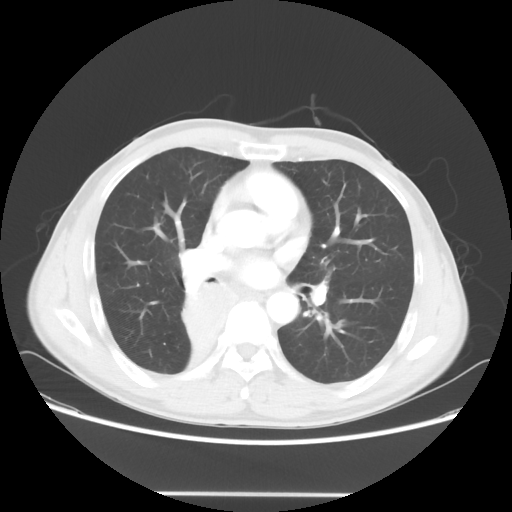
Chest CT, one axial slice; slice 33 of 62 in the series (ordered by position); reconstruction kernel STANDARD; lung window (W 1500 / L -600 HU); 512 × 512 image matrix. Patient: male, 47 years. Case-level facts recorded for this patient, not image findings: clinical TNM (as recorded): T2 N0 M0; histopathological grade: G2.
Outlined on this slice (bounding box drawn by a radiologist):
- lung tumour (recorded histology: squamous cell carcinoma): bounding box [x1, y1, x2, y2] px = [174, 274, 231, 369]